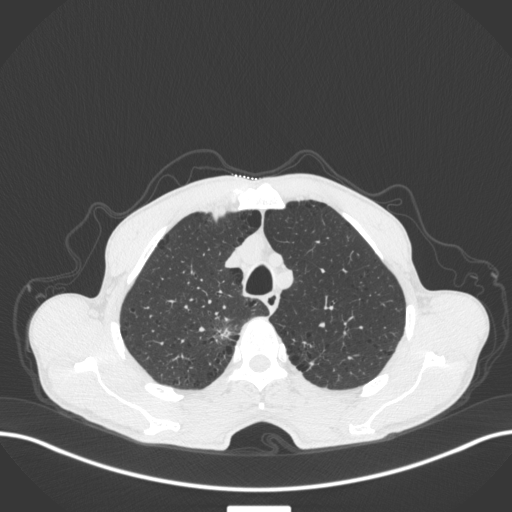
Chest CT, one axial slice; position 344 of 445 along the scan axis; 120 kVp; lung window (W 1500 / L -600 HU); 1 mm slice thickness; 512 × 512 image matrix, field of view 400 × 400 mm. Male patient, age 70 years. Case-level facts recorded for this patient, not image findings: clinical TNM (as recorded): T1a N0 M0.
Outlined on this slice (rectangle marked by the reading radiologist):
- lung tumour (recorded histology: adenocarcinoma): bounding box (x1, y1, x2, y2) in pixels: (213, 314, 237, 349)